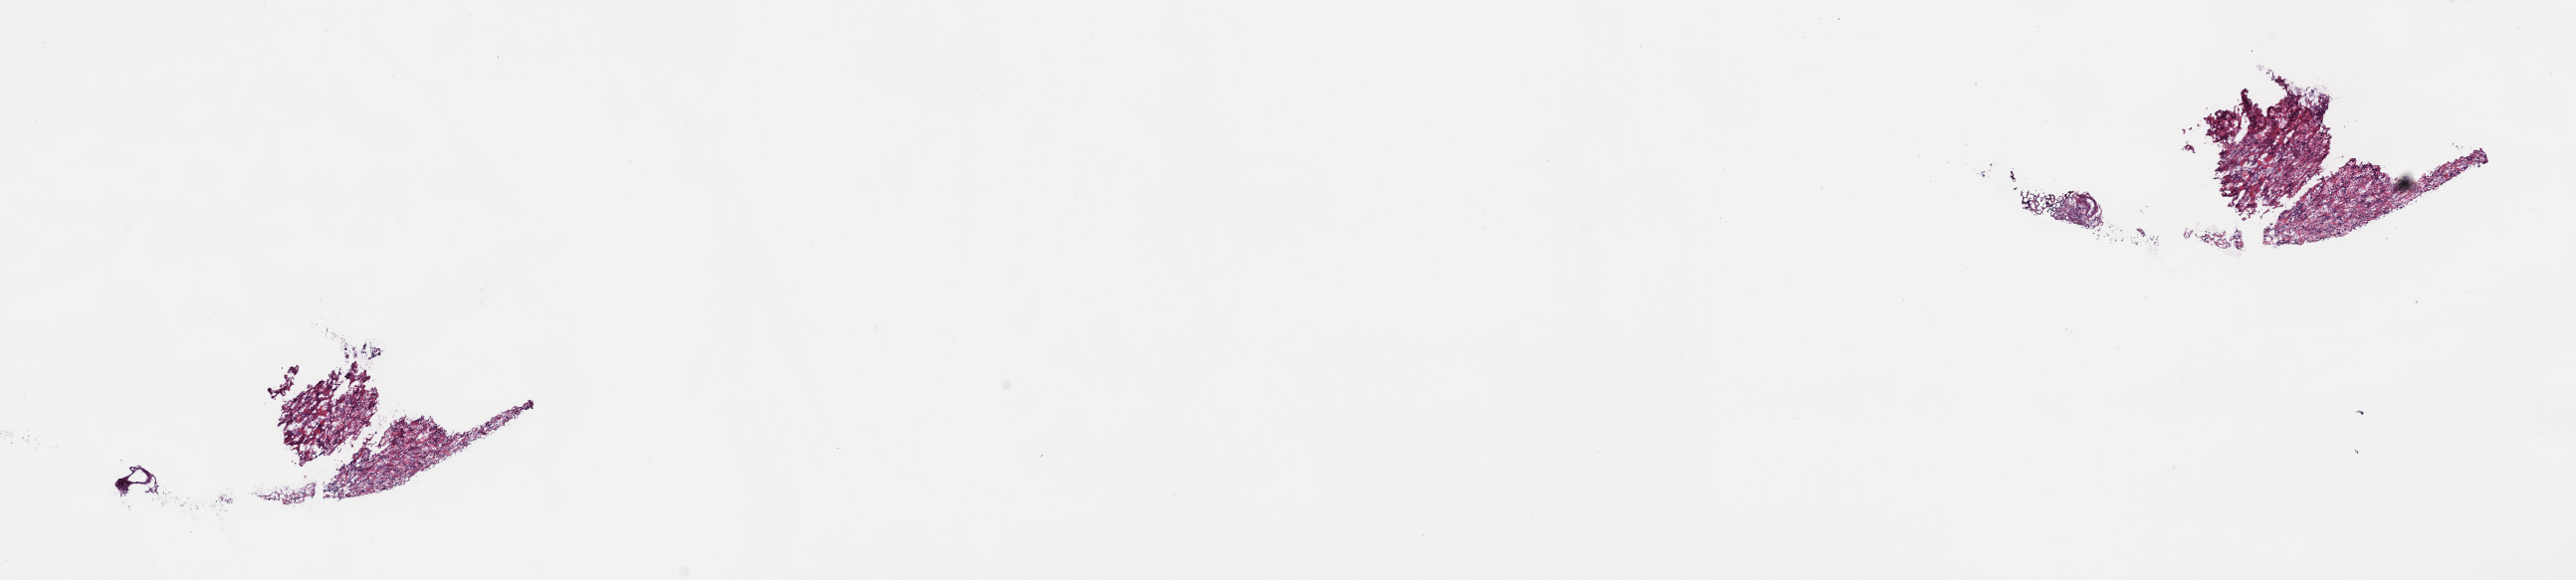
Digitized H&E tissue section (whole slide), whole scanned area (about 20.4 x 4.6 mm, slide scanned at 40x) shown as a low-resolution overview. Frozen section. Stomach, primary tumour sample. Patient: female, age at initial diagnosis 60 years. Pathologist review of this section (percent, as recorded): tumour cells 100%, tumour nuclei 35%.
Histologic diagnosis: Carcinoma, diffuse type (gastric antrum).